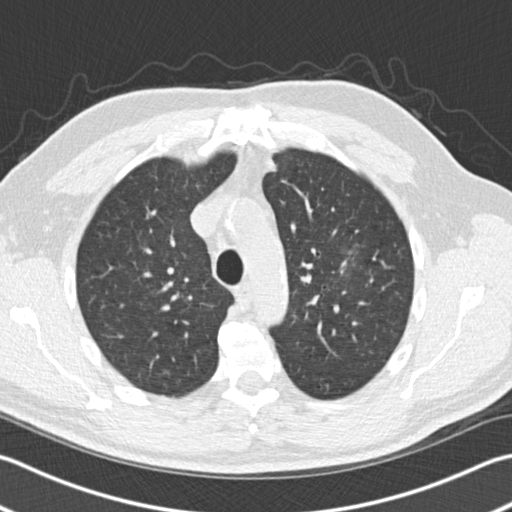
Axial slice from a low-dose chest CT screening exam, third screening round (two years after baseline), lung window (W 1500 / L -600 HU), 2 mm slice thickness, 120 kVp, slice 39 of 153 in the series, 512 × 512 image matrix, field of view 346 × 346 mm. Male participant, aged 65 years at enrolment. Former smoker at enrolment.
- Expert-annotated lung lesion, bounding box (x1, y1, x2, y2) in pixels: (305, 241, 370, 307).
- The screening reader recorded 4 non-calcified nodules or masses ≥4 mm on this exam (left upper lobe, left upper lobe, left lower lobe, right middle lobe); which of them this box marks is not recorded.
- Participant outcome: lung cancer diagnosed 196 days after this screen — acinar cell carcinoma, left upper lobe, stage IA (AJCC 6th edition), 25 mm at pathology.